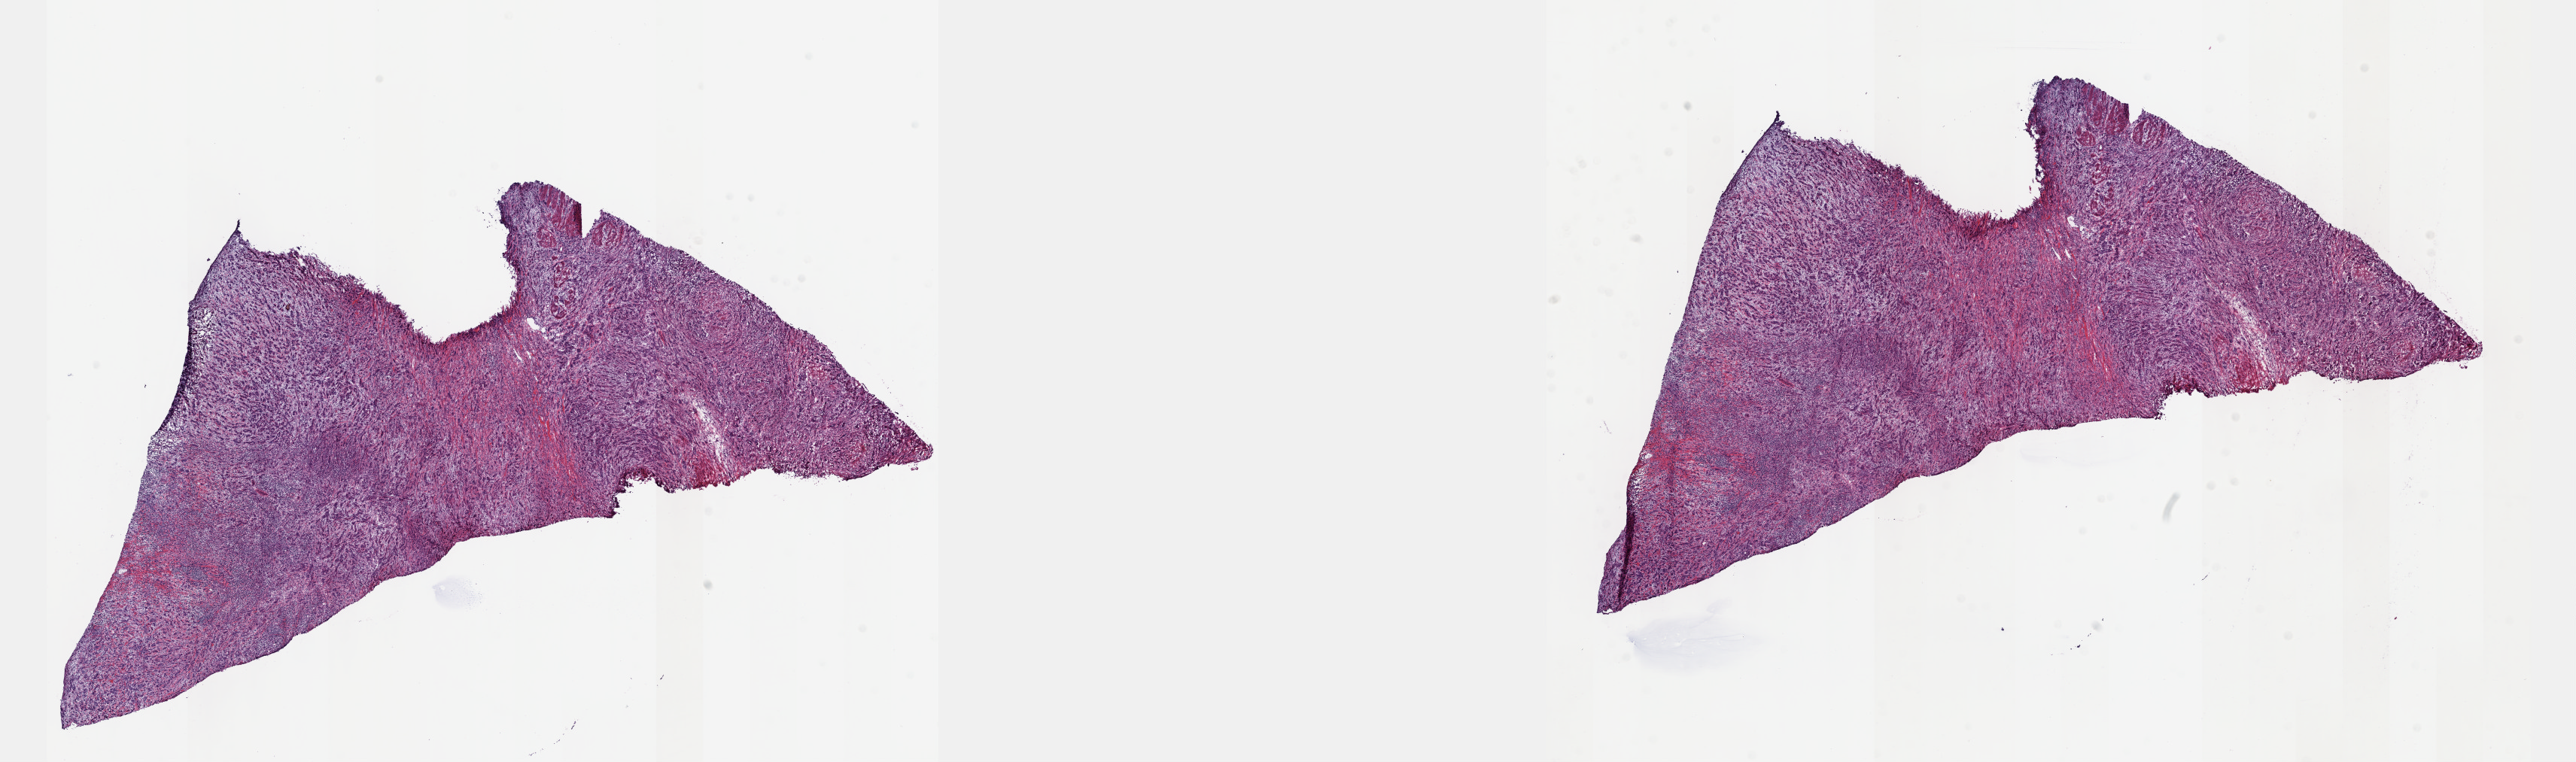
H&E whole-slide image — low-resolution overview of the scanned area, about 27.7 x 8.2 mm, frozen section from the top of the tissue portion, sample: primary tumour, bladder. Patient: female, age at initial diagnosis 63 years. Histologic grade: high grade. Slide review estimates, as recorded: tumour cells 50%, tumour nuclei 60%, normal cells 10%, stromal cells 40%, necrosis 0%. Inflammatory infiltration, as recorded: lymphocyte infiltration 90%, monocyte infiltration 0%, neutrophil infiltration 0%.
* AJCC pathologic stage: IV (6th edition)
* diagnosis: Transitional cell carcinoma
* lymph nodes positive (case pathology): 6 of 71 examined
* TNM: T3b N2 MX